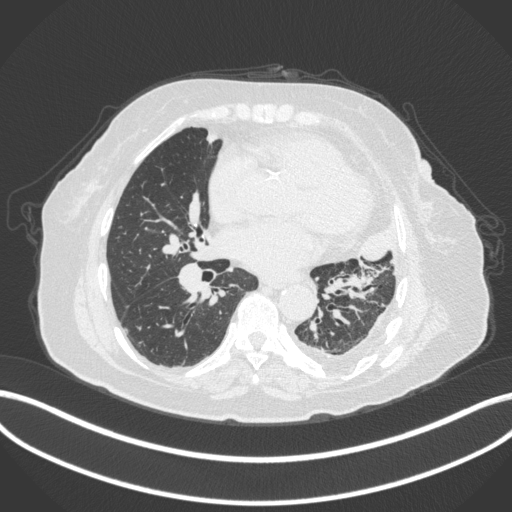
Chest CT, one axial slice. Reconstruction kernel B31f. Lung window (W 1500 / L -600 HU). 1 mm slice thickness. 512 × 512 image matrix, field of view 400 × 400 mm. Female patient, age 75 years. From the clinical record (not read from this slice): clinical TNM (as recorded): T3 N3 M1.
Structures marked on this image (bounding box drawn by a radiologist):
- lung tumour (recorded histology: adenocarcinoma): bounding box [x1, y1, x2, y2] px = [357, 220, 399, 264]